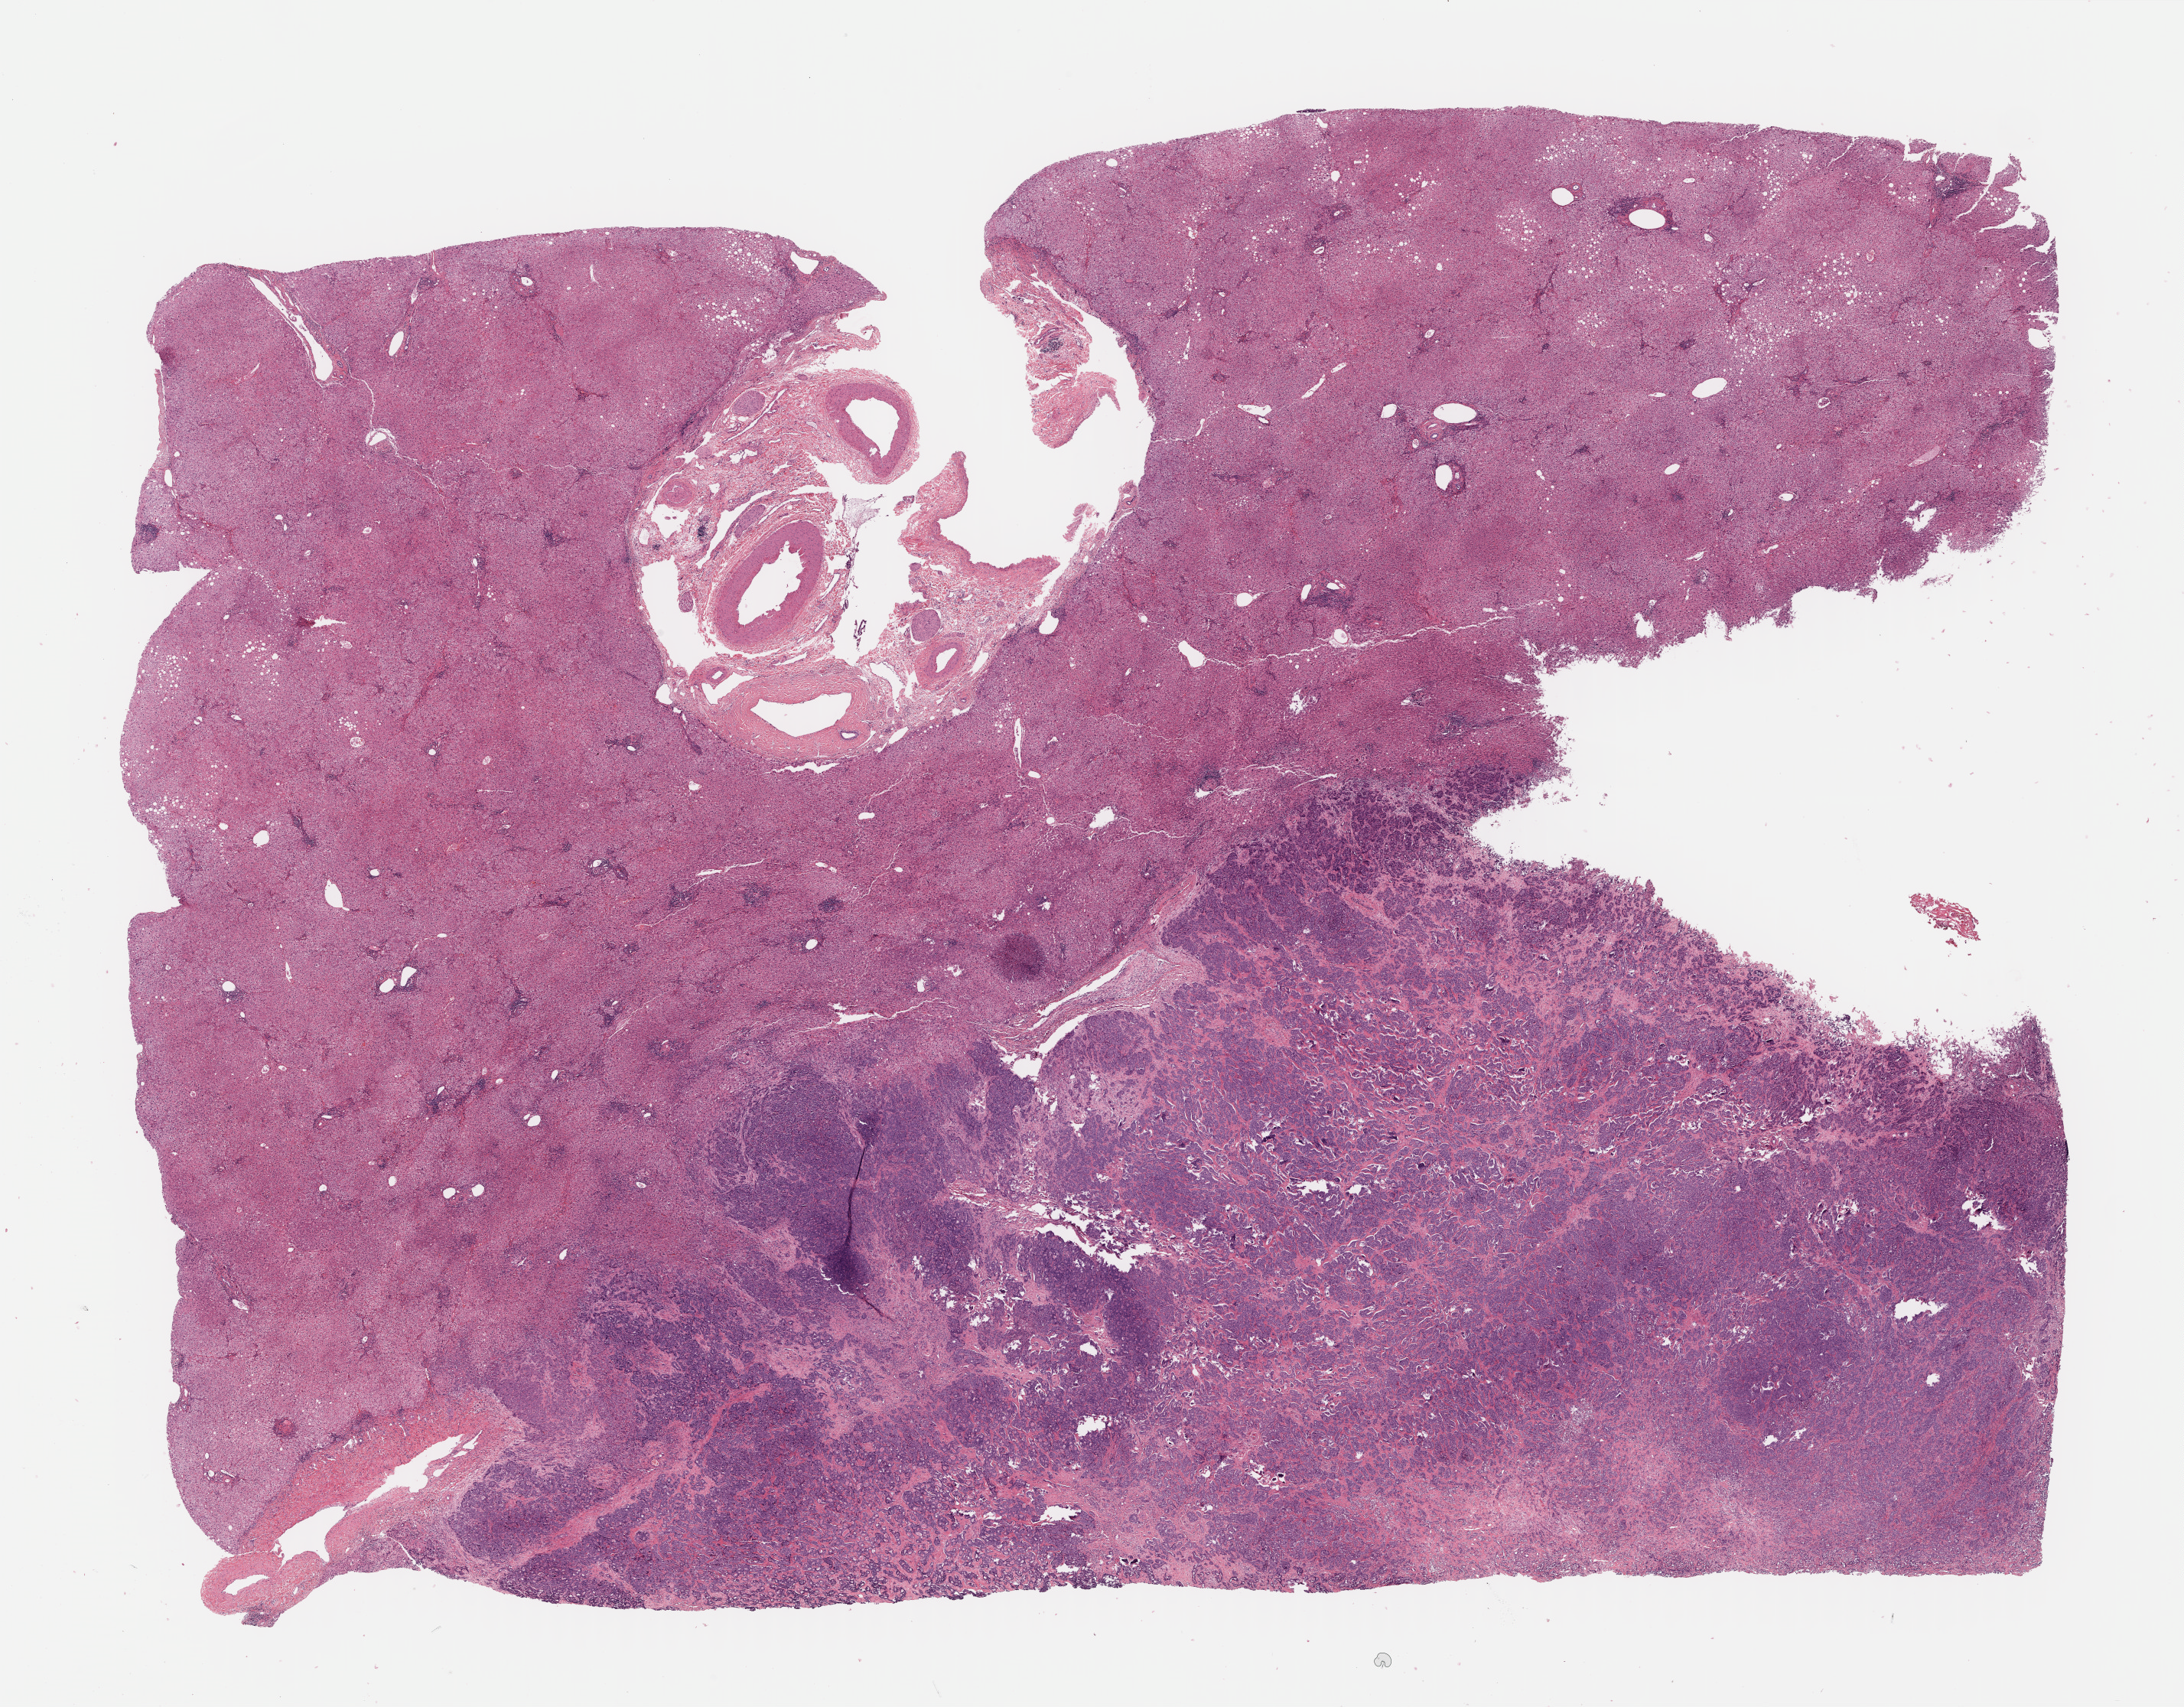
H&E whole-slide image — low-resolution overview of the scanned area, about 23.1 x 18.1 mm (acquisition: 40x scan); formalin-fixed paraffin-embedded (FFPE) diagnostic section; bile duct, primary tumour sample. Female, age 75 years at initial diagnosis. Histologic grade: G2 (moderately differentiated).
Diagnosis: Cholangiocarcinoma (intrahepatic bile duct). AJCC pathologic stage: I (7th edition). TNM: T1 N0 M0.